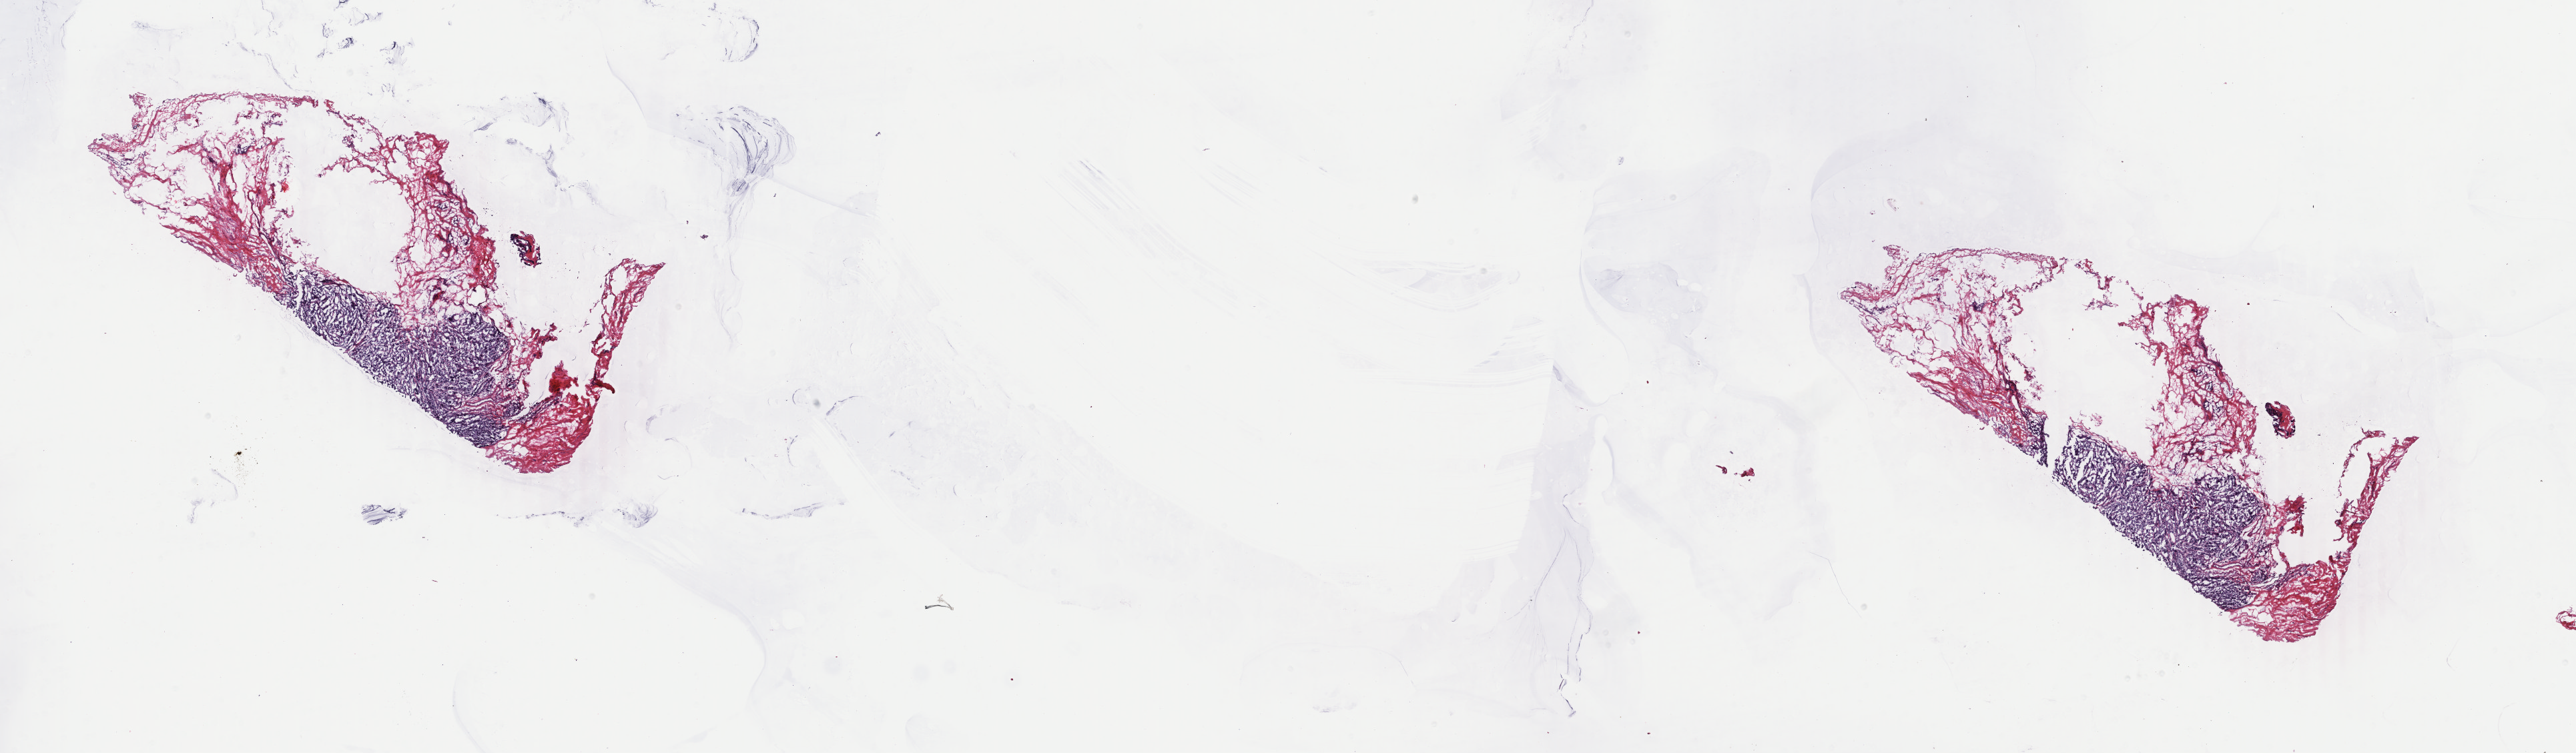
H&E-stained whole-slide image, shown as a low-resolution overview of the whole scanned area (about 30.7 x 9.0 mm), frozen section, primary tumour sample from the breast. Female patient; age at initial diagnosis 56 years. Slide review estimates, as recorded: tumour cells 30%, tumour nuclei 85%.
Diagnosis: Infiltrating duct carcinoma, NOS.